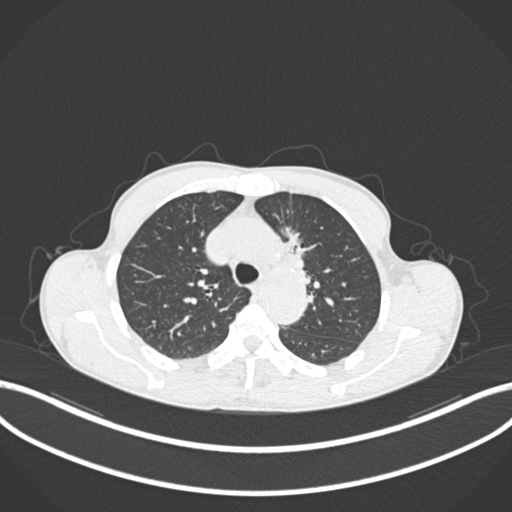
Chest CT, one axial slice; position 142 of 211 along the scan axis; reconstruction kernel B30f; 120 kVp; lung window (W 1500 / L -600 HU); 1 mm slice thickness; 512 × 512 image matrix, field of view 400 × 400 mm. Patient: male, 58 years. From the clinical record (not read from this slice): clinical TNM (as recorded): T1c N1 M0.
Annotated regions visible in this slice (rectangle marked by the reading radiologist):
- lung tumour (recorded histology: adenocarcinoma): bounding box (x1, y1, x2, y2) in pixels: (278, 226, 310, 282)